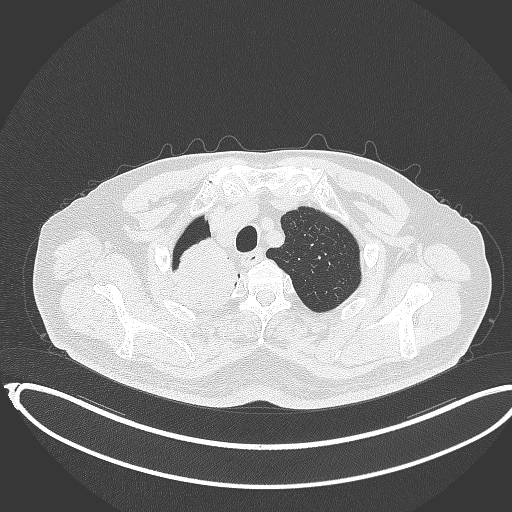
Chest CT, one axial slice. Slice 321 of 403 in the series (ordered by position). Lung window (W 1500 / L -600 HU). 1 mm slice thickness. 512 × 512 image matrix. Male patient, age 68 years. From the clinical record (not read from this slice): clinical TNM (as recorded): T2a N0 M0.
Annotated regions visible in this slice (rectangle marked by the reading radiologist):
- lung tumour (recorded histology: adenocarcinoma): bounding box [x1, y1, x2, y2] px = [164, 235, 242, 320]